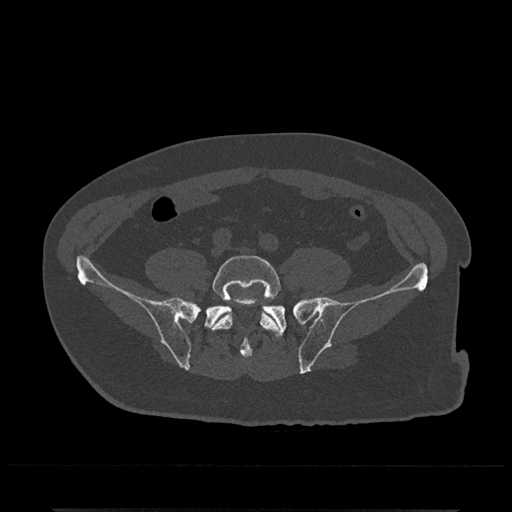
CT including the spine, one axial slice. Position 63 of 797 along the scan axis. Reconstruction kernel Br40s/3. Bone window (W 1800 / L 400 HU). 0.5 mm slice thickness. 512 × 512 image matrix, field of view 393 × 393 mm. Male patient, age 67 years. Case-level facts recorded for this patient, not image findings: primary cancer: prostate.
Outlined on this slice (semi-automatically segmented with operator editing):
- L5 vertebra: bounding box <210,255,280,333> (left, top, right, bottom; pixels)